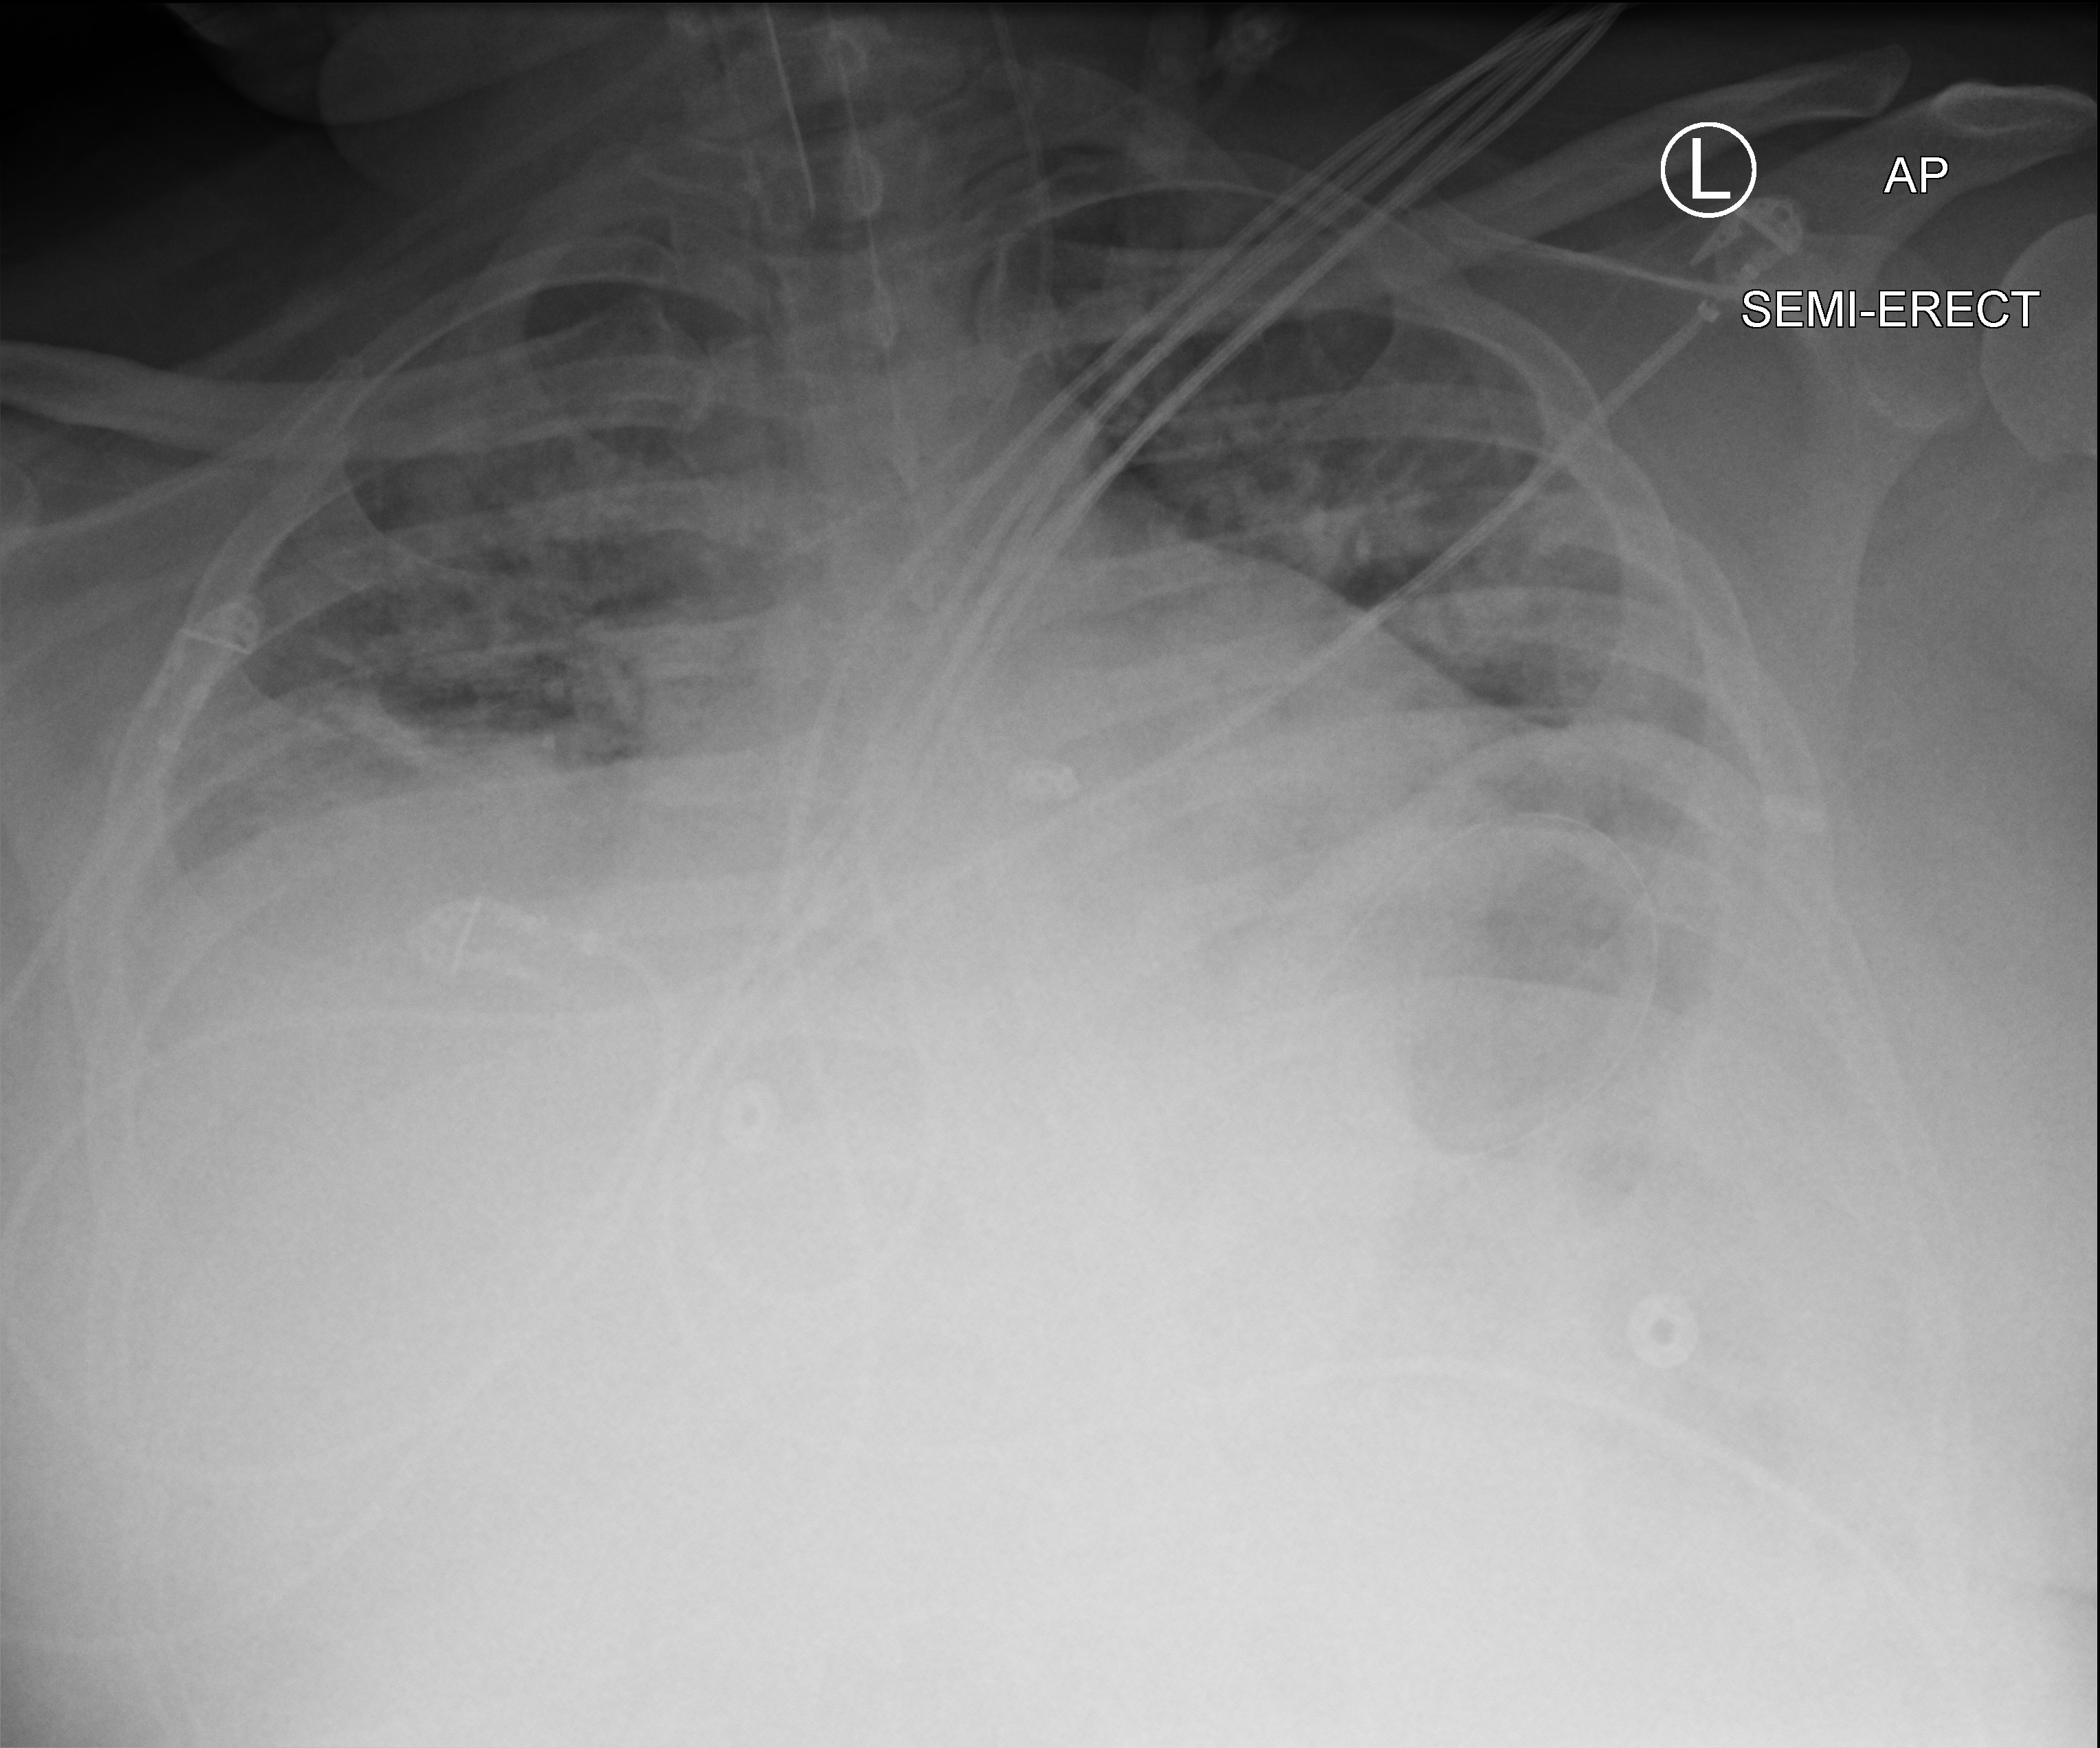
Chest X-ray (portable), anteroposterior (AP) projection. Male patient hospitalised with COVID-19, age 18–59 years.
From the hospital-stay record, not from the radiograph (when in the stay this image was taken is not recorded): mechanically ventilated during this hospital stay: yes; admitted to intensive care during this hospital stay: yes.